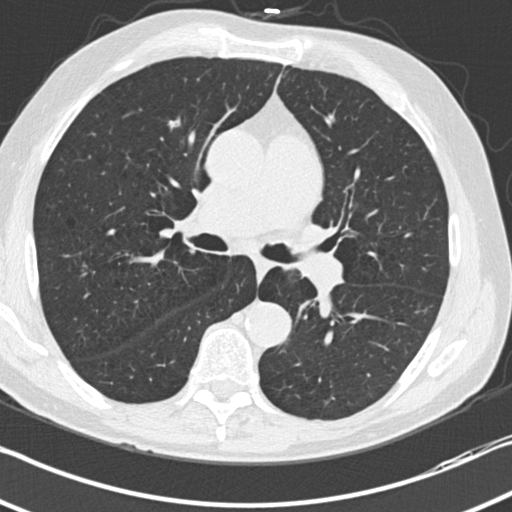
Low-dose screening chest CT, one axial slice; position 124 of 212 along the scan axis; 120 kVp; lung window (W 1500 / L -600 HU); 2 mm slice thickness; 512 × 512 image matrix, field of view 336 × 336 mm.
Outlined on this slice (expert manual segmentation):
- lesion 1 (tumor, upper lobe of right lung): bounding box (x1, y1, x2, y2) in pixels: (169, 119, 180, 128)